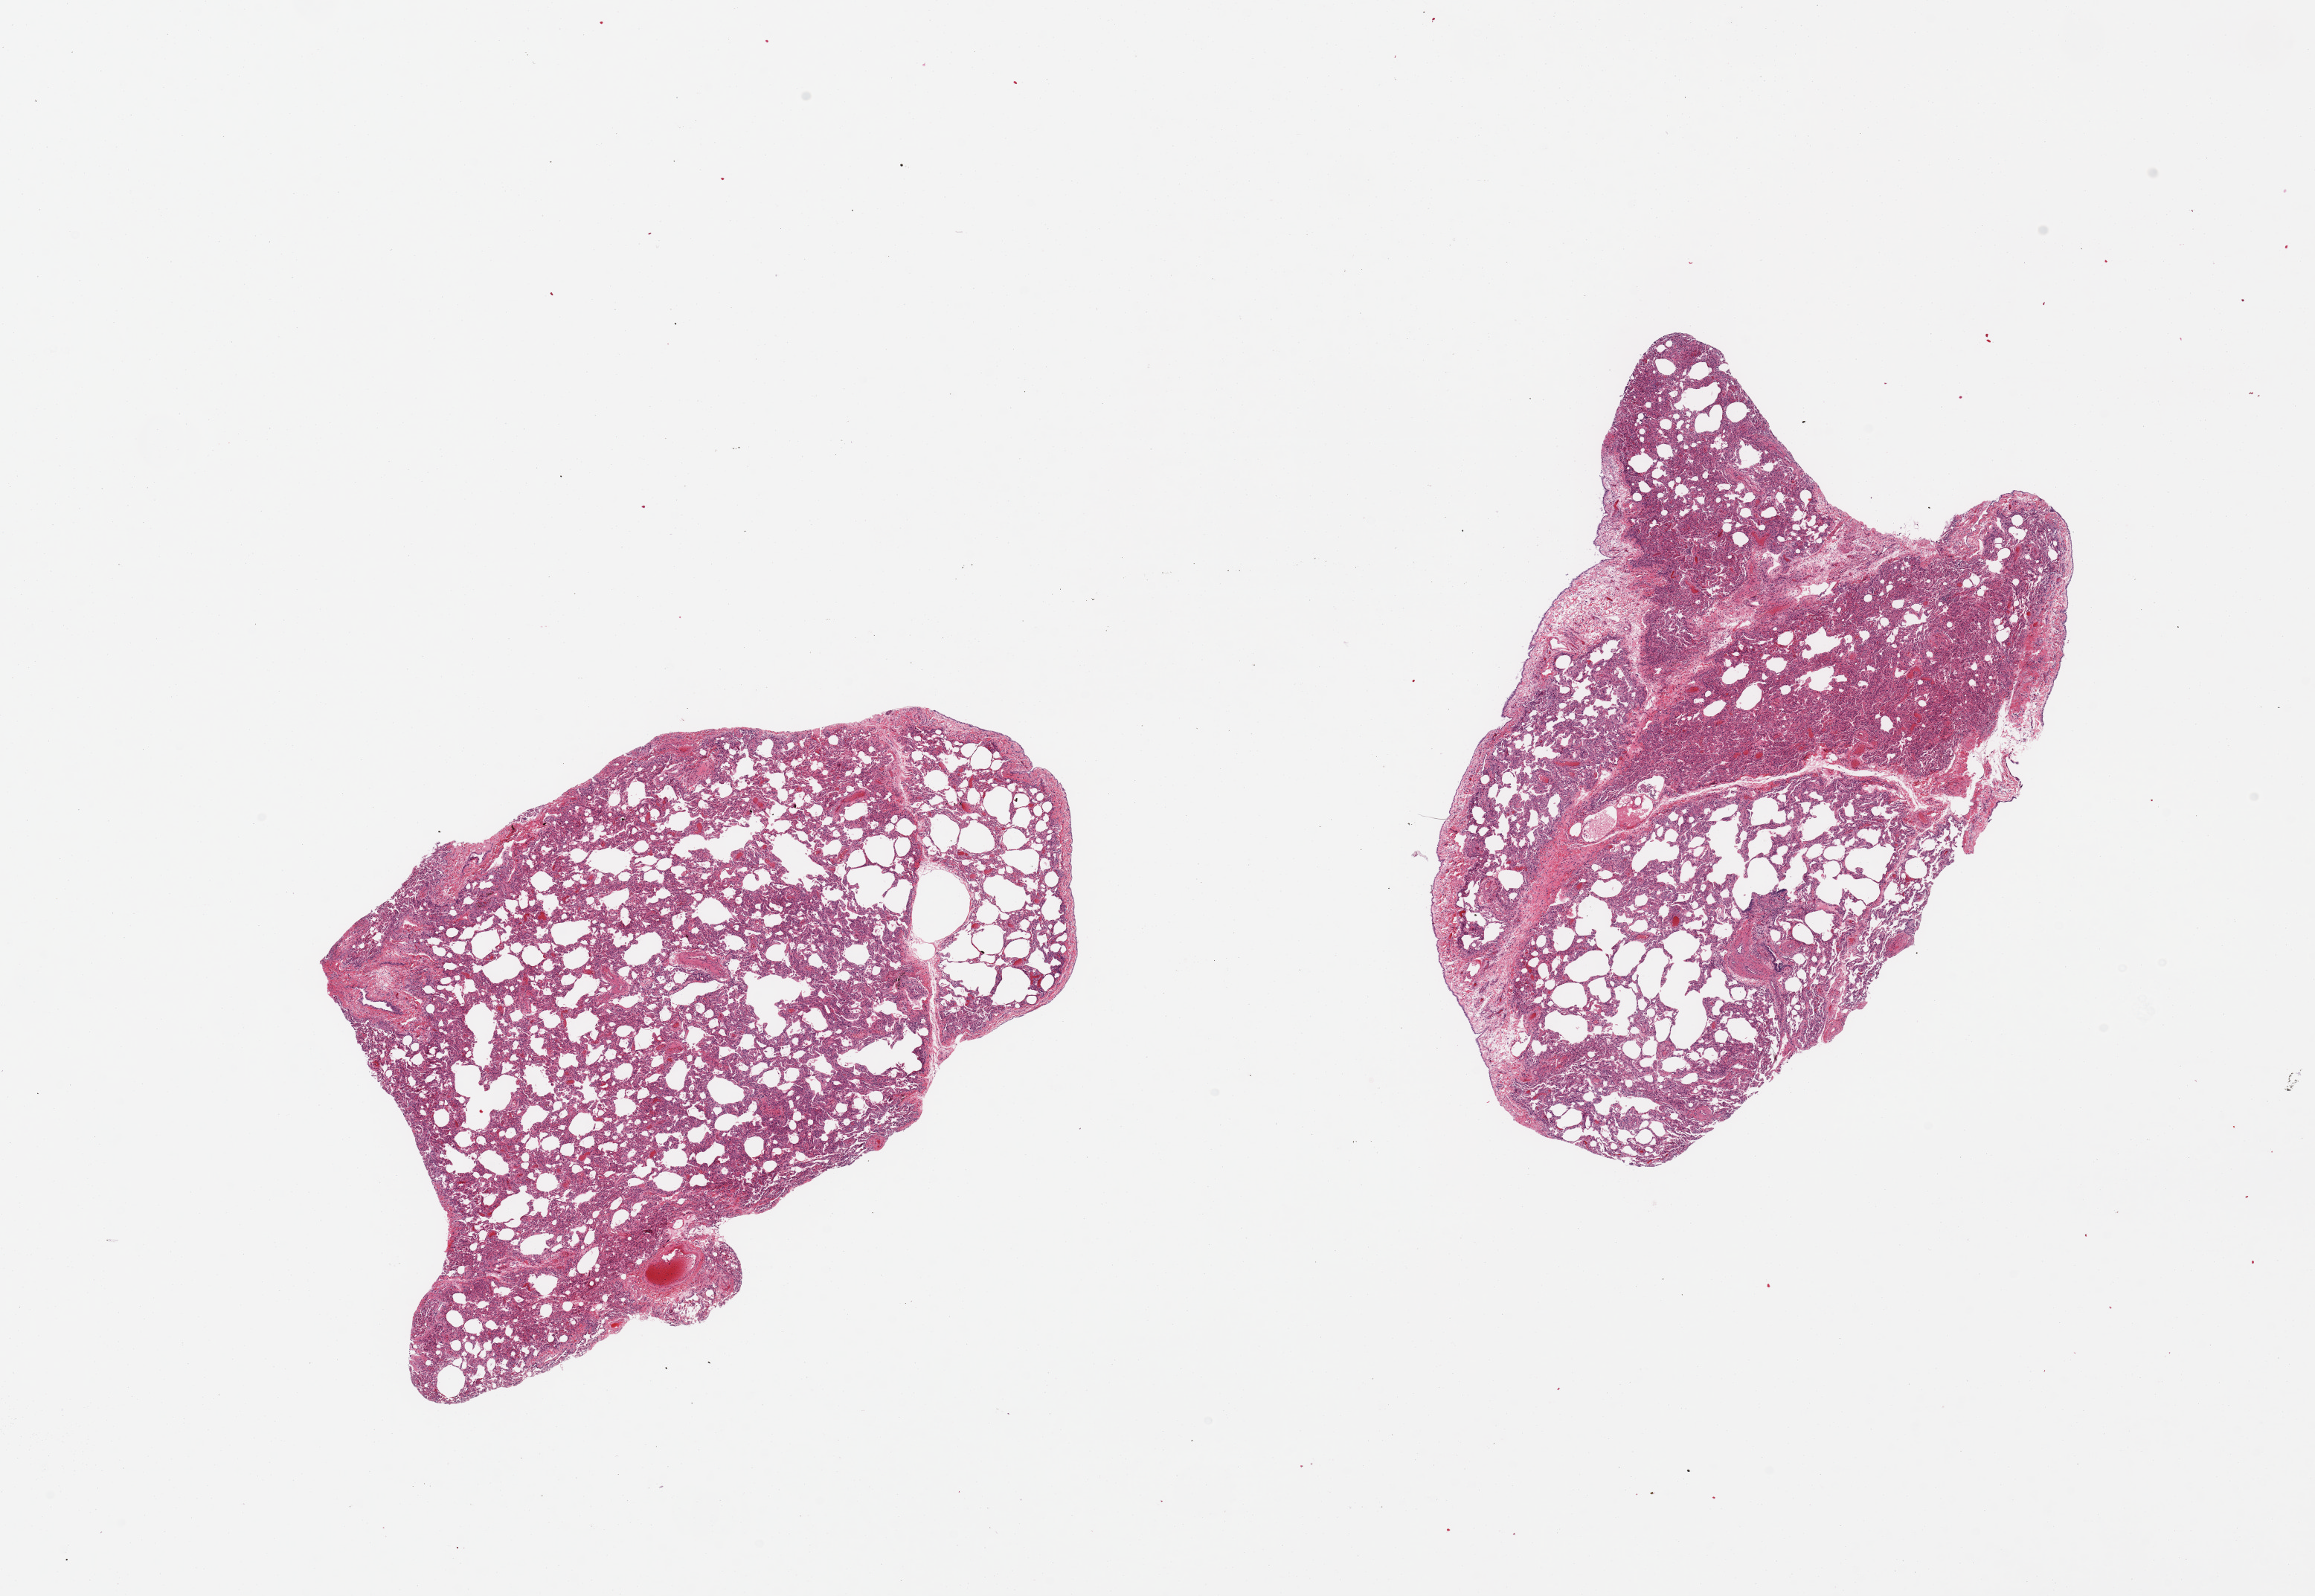
Haematoxylin and eosin whole-slide image — shown as a low-resolution overview of the whole scanned area (about 24.6 x 17.0 mm), PAXgene-fixed paraffin-embedded (PFPE) section, target tissue: lung, donor tissue sample. Donor: male.
Pathologist's review note for this sample: 2 pieces; includes pleura (target is 1cm below pleura), collapse and some emphysematous change, pneumonia.